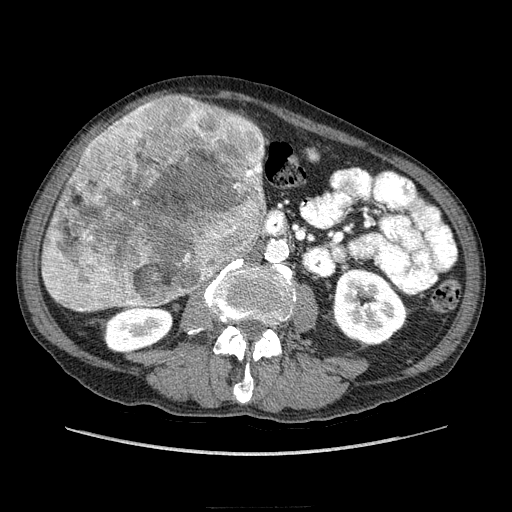
Contrast-enhanced abdominal CT (liver protocol), one axial slice. Slice 73 of 218 in the series (ordered by position). Reconstruction kernel STANDARD. Soft-tissue window (W 400 / L 40 HU). 512 × 512 image matrix, field of view 380 × 380 mm. Case-level facts recorded for this patient, not image findings: diagnosis: hepatocellular carcinoma (patient treated with transarterial chemoembolisation; whether this scan precedes or follows treatment is not stated here); TNM stage (as recorded): Stage-IIIA; Child-Pugh class: A; tumour differentiation: well differentiated; tumour size: 20 cm.
Outlined on this slice (semi-automatic segmentation, software-assisted and operator-edited):
- liver parenchyma outside the tumour (the mass and vessels are separate outlines, so this box may not span the whole liver): bounding box [x1, y1, x2, y2] px = [42, 99, 195, 312]
- mass: [43, 96, 268, 311]